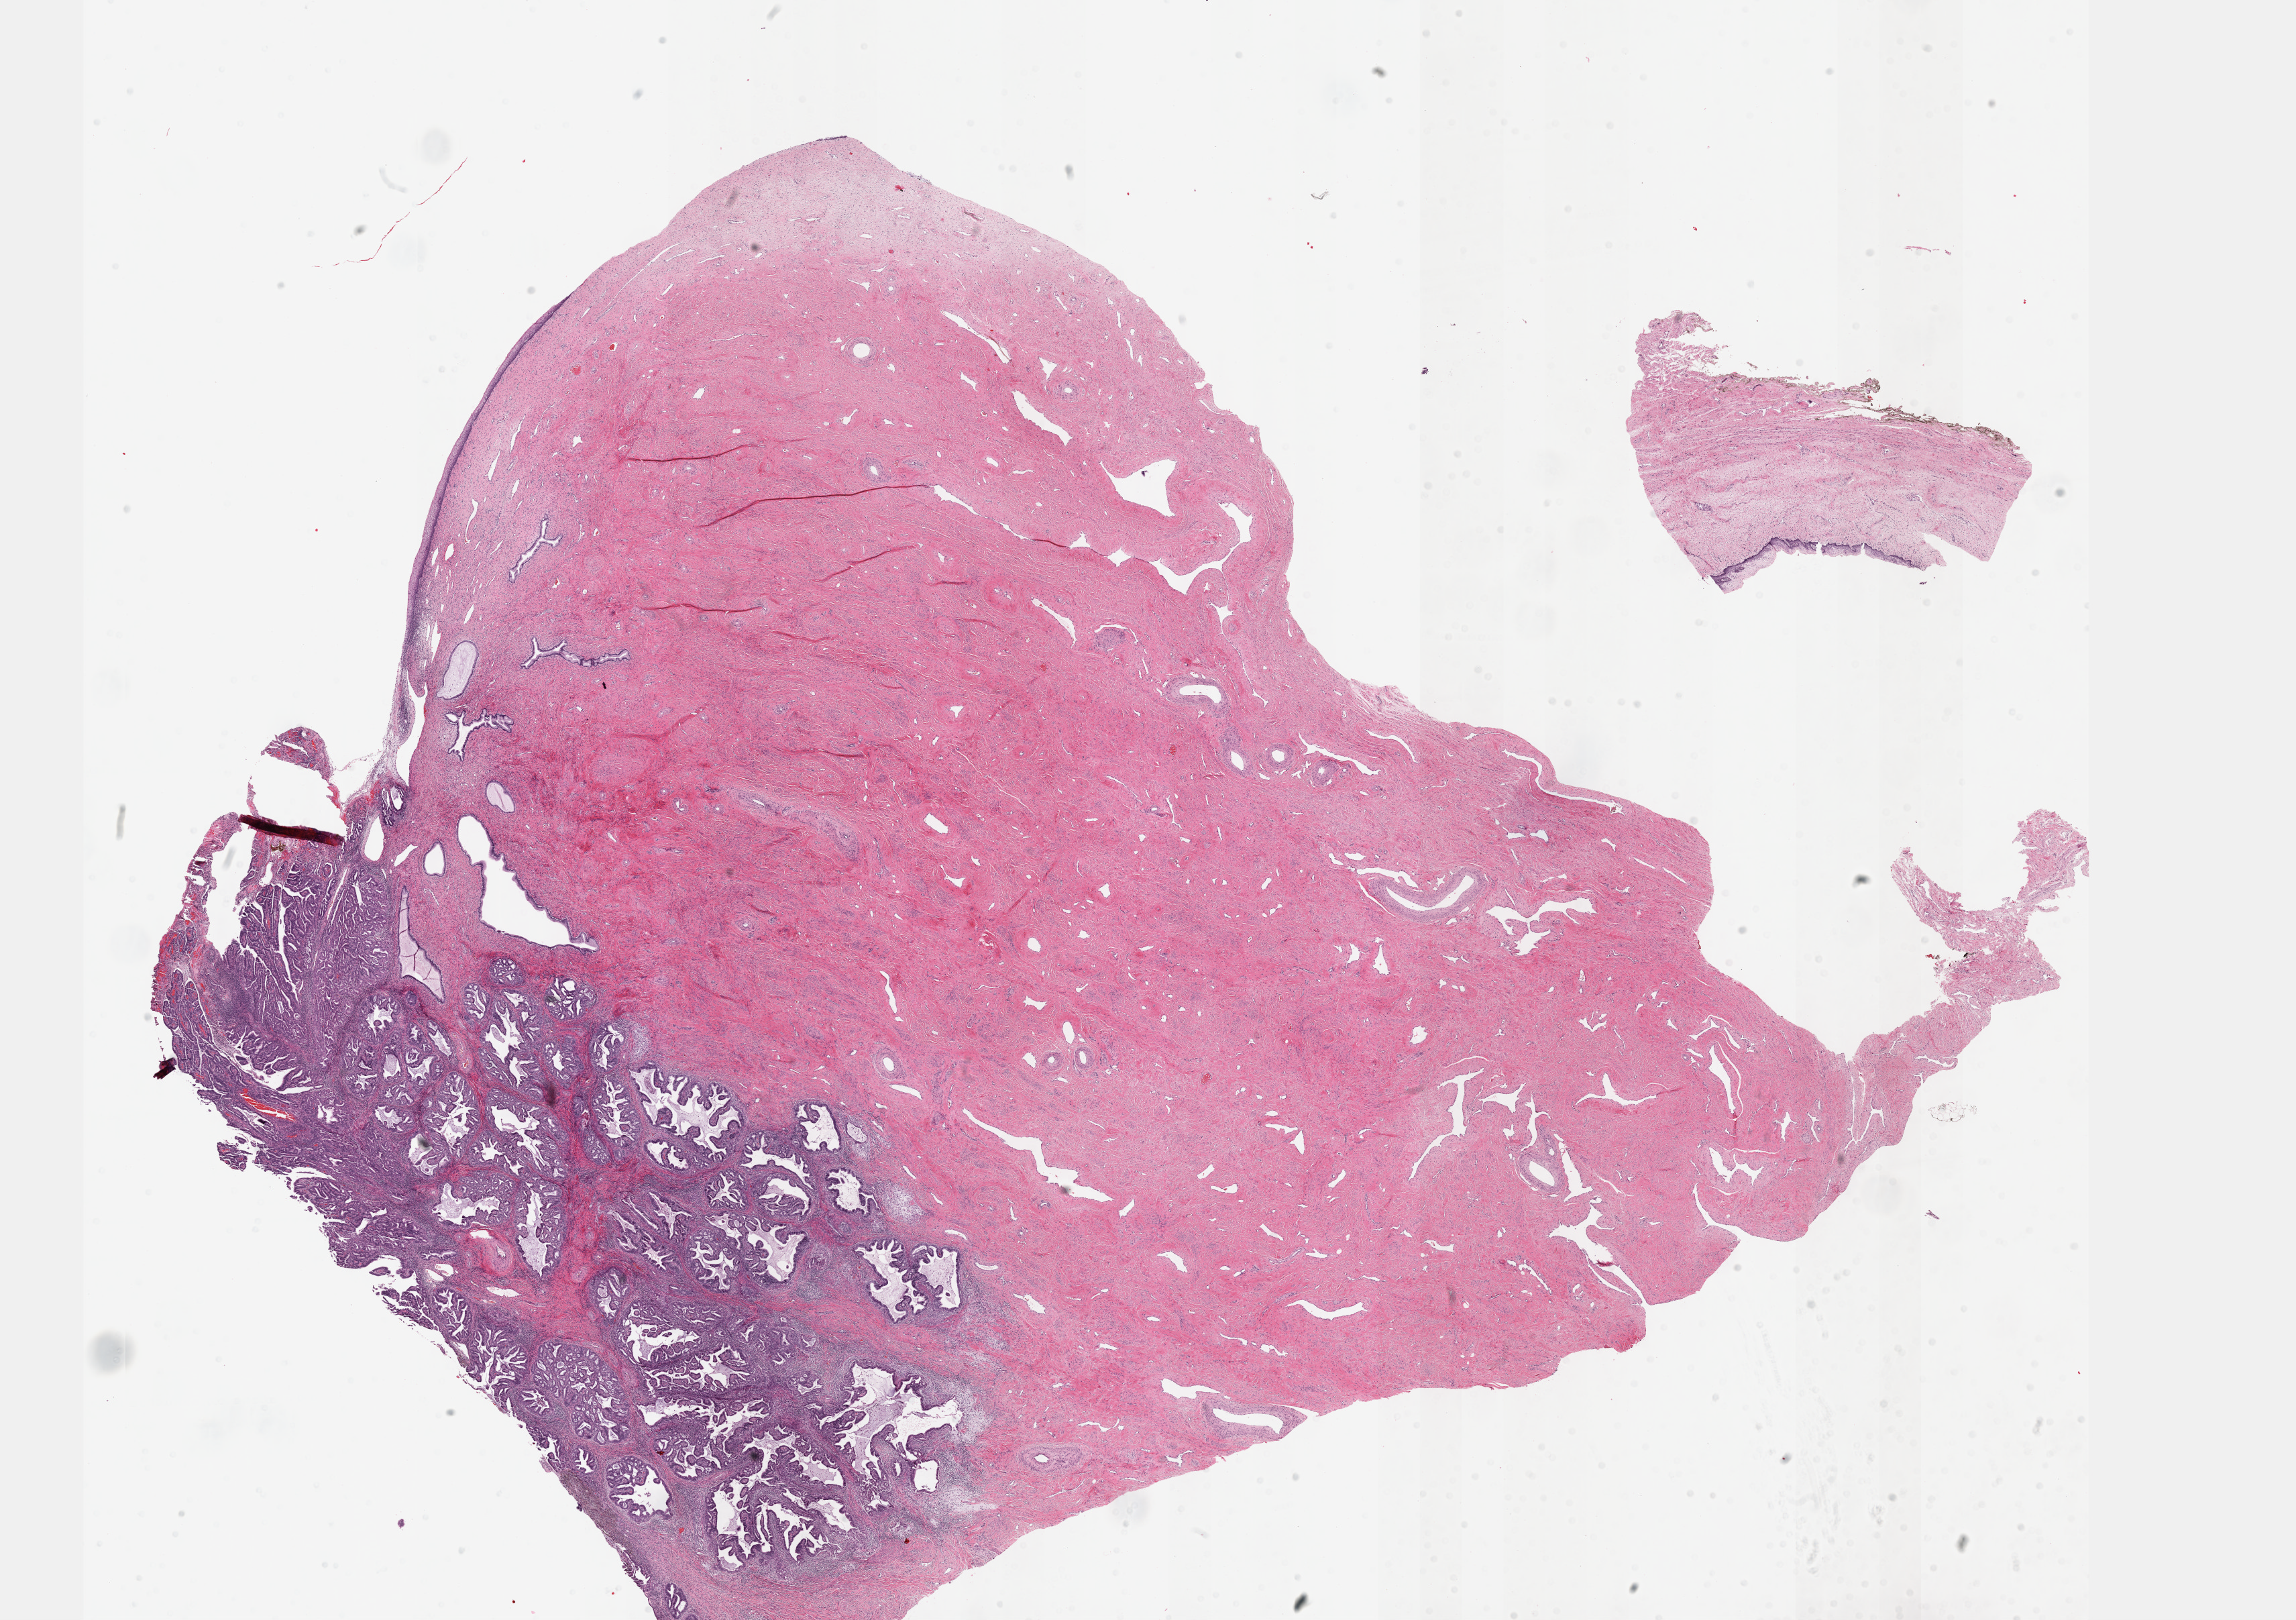
H&E whole-slide image — whole scanned area (about 27.7 x 19.5 mm, acquisition: 40x scan) shown as a low-resolution overview; formalin-fixed paraffin-embedded (FFPE) diagnostic section; primary tumour sample from the cervix. Female patient; age at initial diagnosis 45 years. Histologic grade: G1 (well differentiated).
FIGO stage: IB1. Lymph nodes positive (case pathology): 0 of 17 examined. Histologic diagnosis: Adenocarcinoma, endocervical type (cervix uteri).